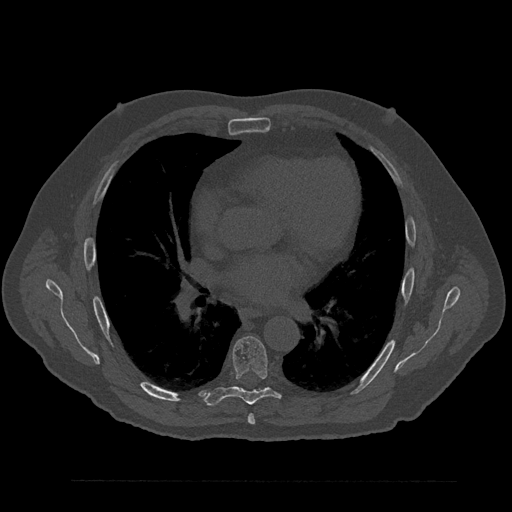
CT including the spine, one axial slice; position 508 of 797 along the scan axis; 120 kVp; bone window (W 1800 / L 400 HU); 0.5 mm slice thickness; 512 × 512 image matrix. Patient: male, 61 years. Case-level facts recorded for this patient, not image findings: primary cancer: prostate.
Structures marked on this image (semi-automatically segmented with operator editing):
- T6 vertebra: bounding box (x1, y1, x2, y2) in pixels: (248, 414, 255, 425)
- T7 vertebra: (204, 336, 281, 405)